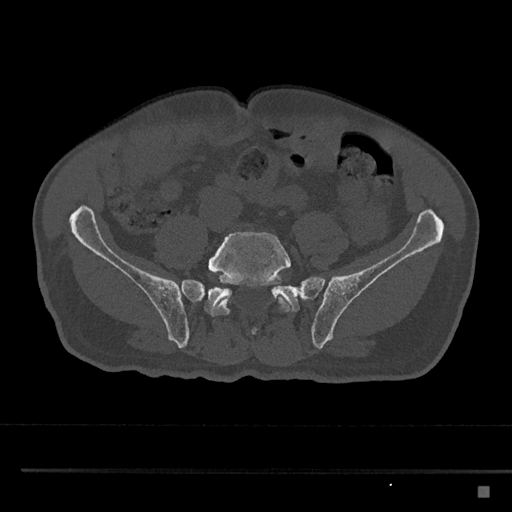
CT including the spine, one axial slice; slice 564 of 797 in the series (ordered by position); 120 kVp; bone window (W 1800 / L 400 HU); 0.5 mm slice thickness; 512 × 512 image matrix, field of view 391 × 391 mm. Patient: male, 59 years. From the clinical record (not read from this slice): primary cancer: prostate.
Outlined on this slice (semi-automatic segmentation, software-assisted and operator-edited):
- L5 vertebra: box from (x=208, y=231) to (x=291, y=335) px